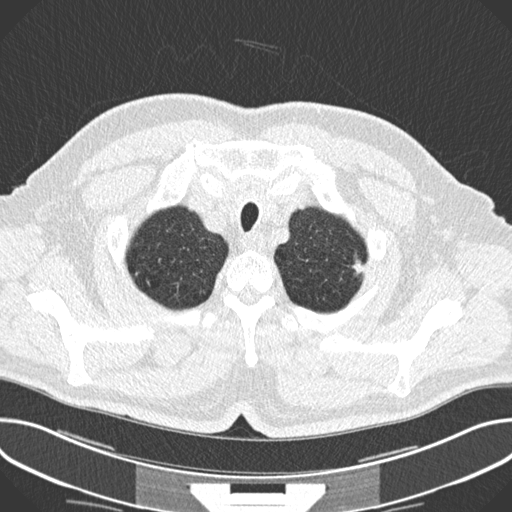
Low-dose screening chest CT, axial slice. Baseline screening round. Lung window (W 1500 / L -600 HU). 2 mm slice thickness. Slice 25 of 245 in the series. 512 × 512 image matrix. Male, age 63 years at enrolment.
Expert reader's lesion annotation, bounding box [x1, y1, x2, y2] px = [343, 250, 384, 283]. The screening reader recorded 2 non-calcified nodules or masses ≥4 mm on this exam; which of them this box marks is not recorded. Official screen result: positive, change unspecified: nodule(s) >= 4 mm or enlarging nodule(s), mass(es), or other non-specific abnormalities suspicious for lung cancer. Lung cancer was diagnosed 174 days after this screen: adenocarcinoma, NOS, left upper lobe, poorly differentiated (G3), stage IIIA (AJCC 6th edition), 11 mm at pathology.